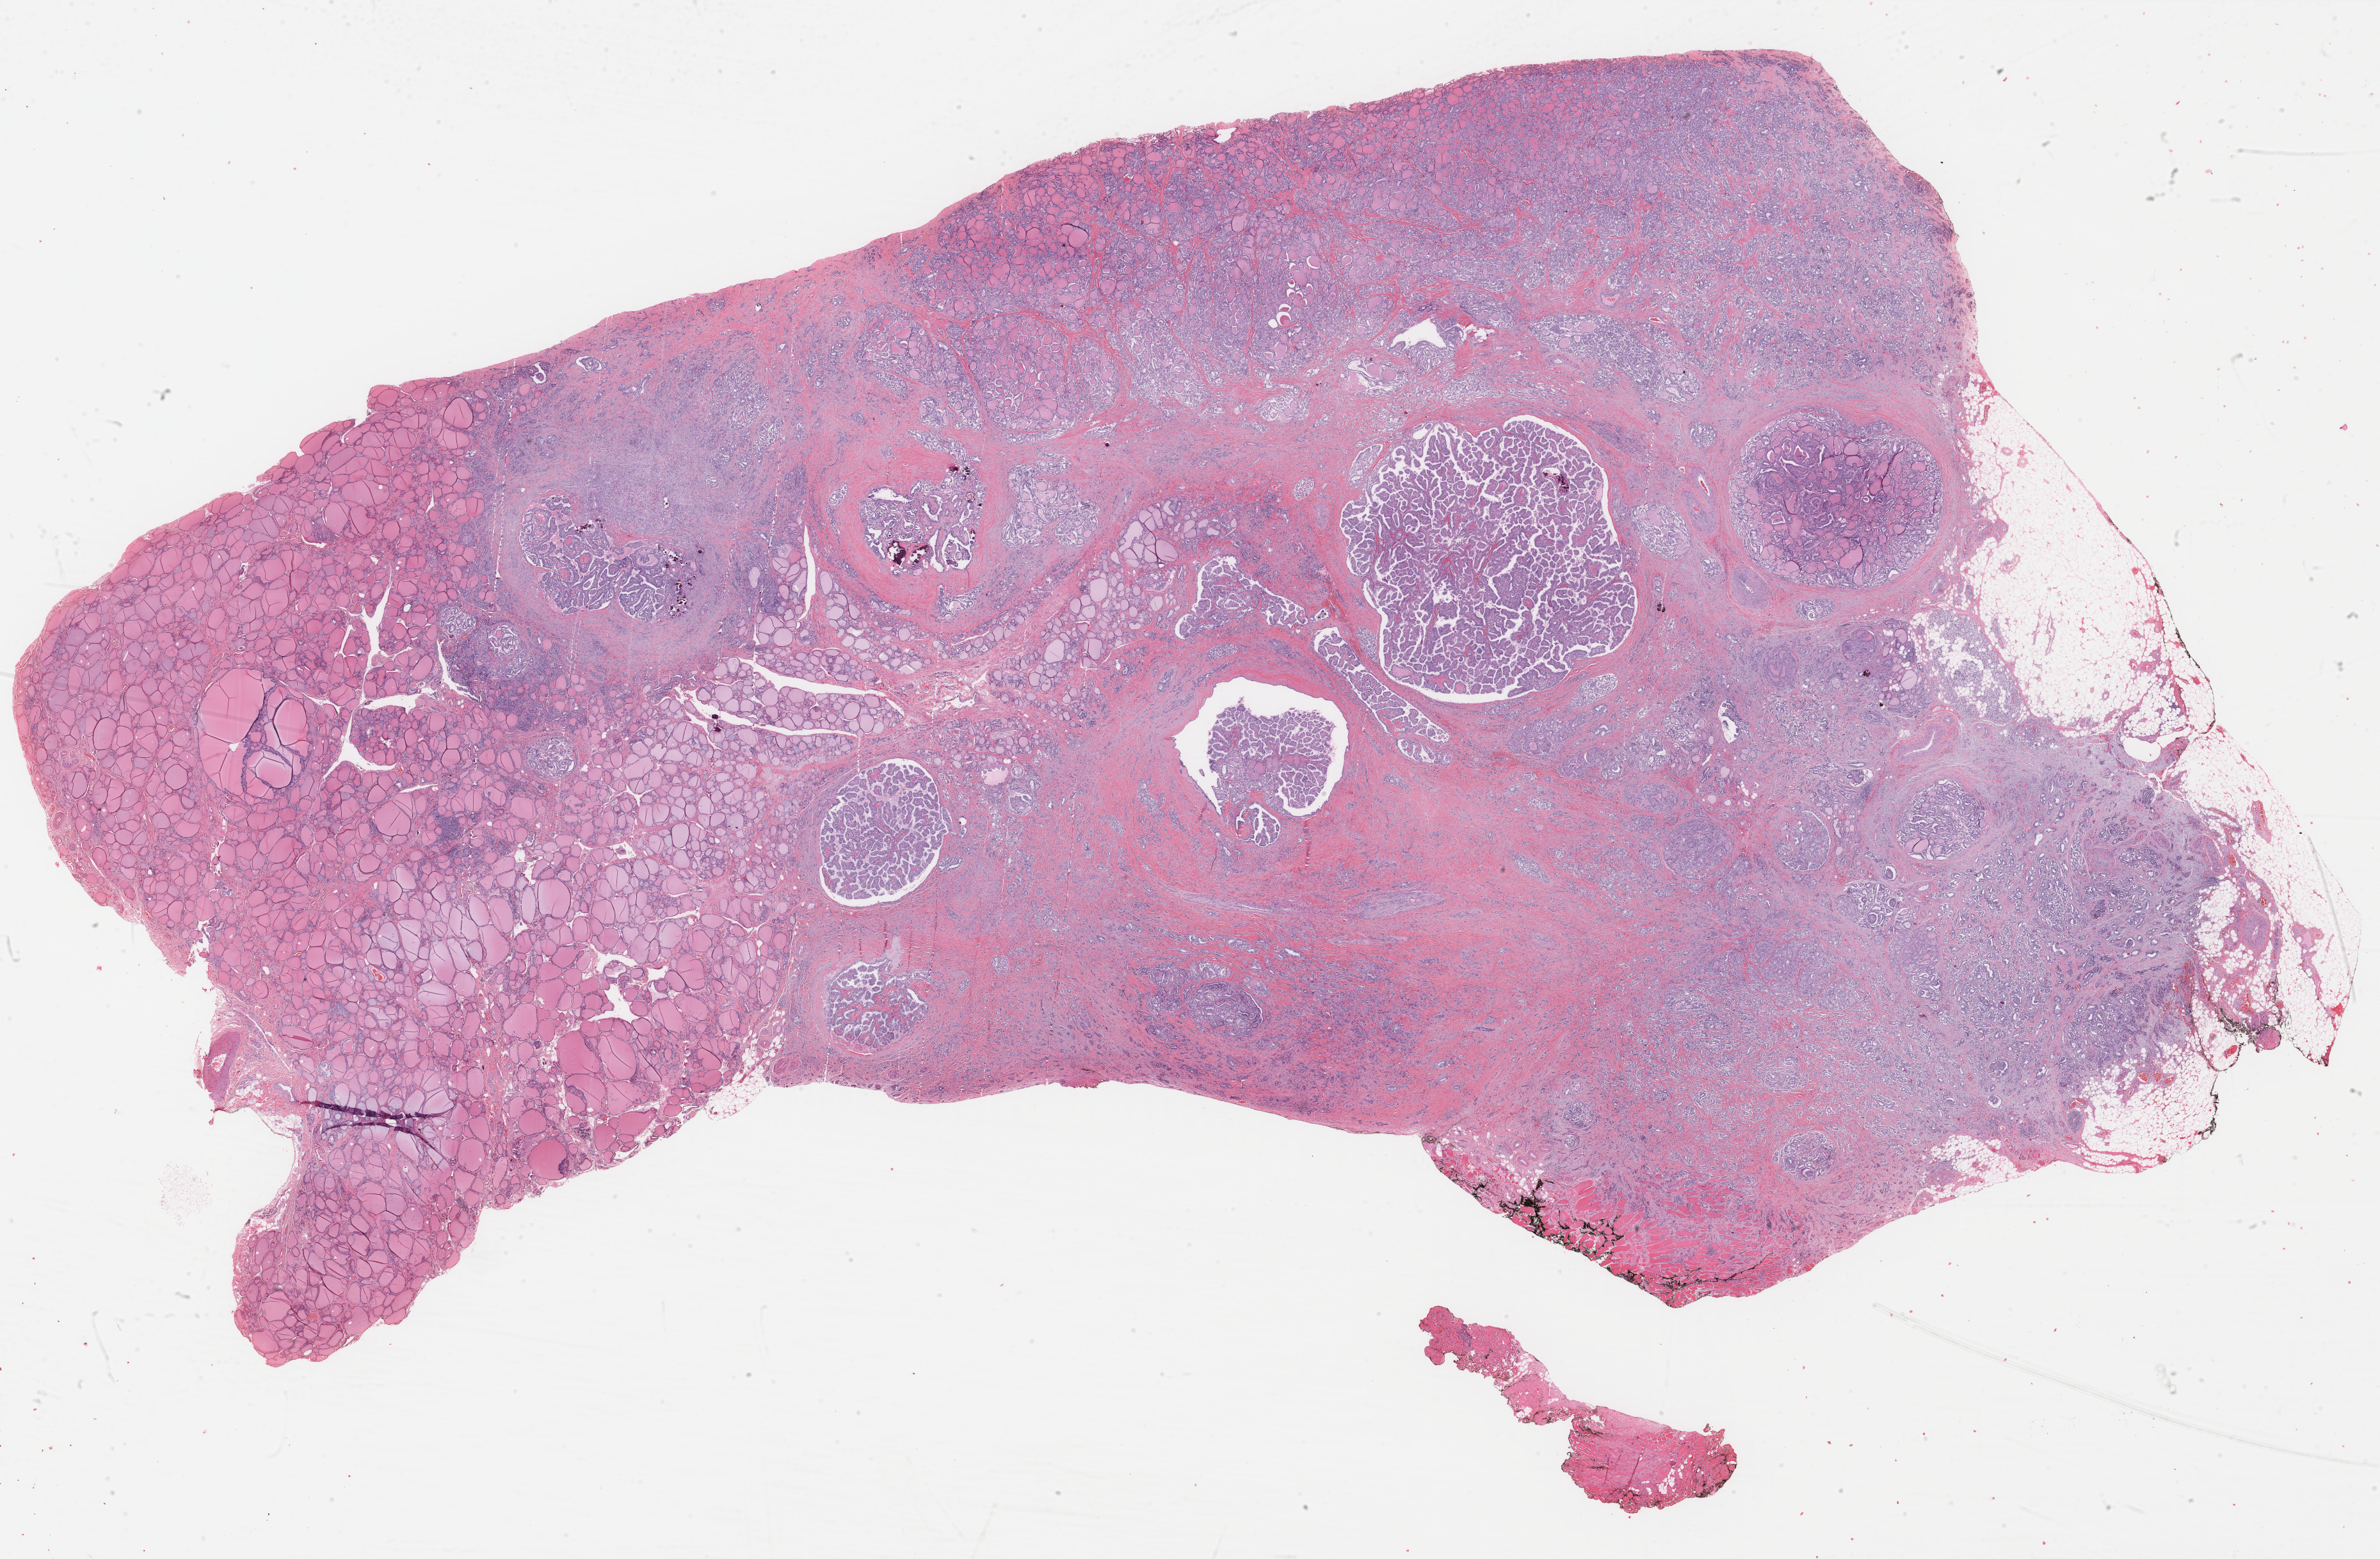
Digitized H&E-stained tissue section (whole slide) — low-resolution overview of the scanned area, about 29.5 x 19.3 mm (from a 40x scan). Formalin-fixed paraffin-embedded (FFPE) diagnostic section. Sample: primary tumour, thyroid. Patient: male, age at initial diagnosis 61 years.
AJCC pathologic stage: III (5th edition). Pathologic diagnosis: Papillary adenocarcinoma, NOS (thyroid gland). TNM: T4 N1b M0.